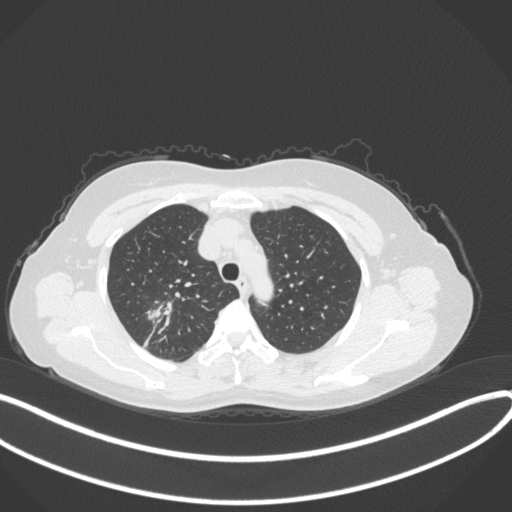
Chest CT, one axial slice. Slice 284 of 342 in the series (ordered by position). Lung window (W 1500 / L -600 HU). 512 × 512 image matrix. Female patient, age 50 years. From the clinical record (not read from this slice): clinical TNM (as recorded): T1c N0 M0; histopathological grade: G2-3.
Outlined on this slice (bounding box drawn by a radiologist):
- lung tumour (recorded histology: adenocarcinoma): bounding box (x1, y1, x2, y2) in pixels: (140, 304, 171, 325)